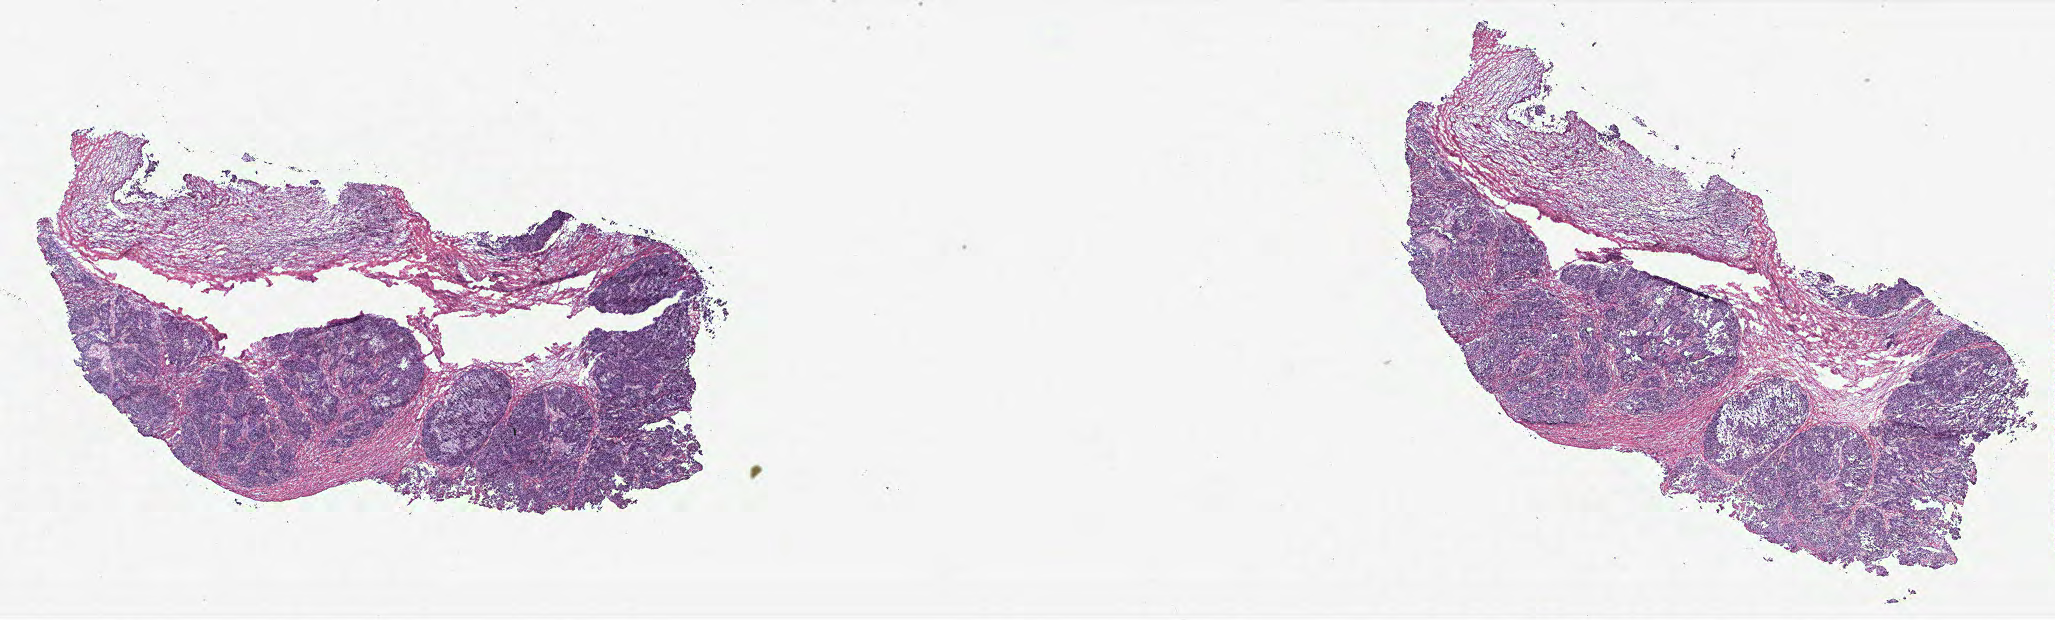
Digitized H&E tissue section (whole slide) — whole scanned area (about 32.9 x 9.9 mm) shown as a low-resolution overview. Ovary, tissue type not recorded.
- patient diagnosis (cohort enrolment): ovarian cancer (ovary)